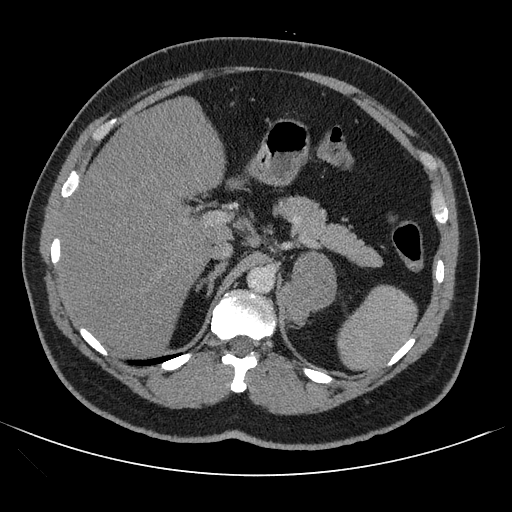
Contrast-enhanced abdominal CT, one axial slice. Slice 72 of 121 in the series (ordered by position). 120 kVp. Intravenous contrast given. Soft-tissue window (W 400 / L 40 HU). 2.5 mm slice thickness. 512 × 512 image matrix, field of view 399 × 399 mm. Male patient, age 53 years. From the clinical record (not read from this slice): diagnosis: adrenocortical carcinoma; tumour side: left adrenal; tumour size at pathology: 7.9 cm; Ki-67 index: 20 %; stage (as recorded): 2.
Structures marked on this image (semi-automatically segmented with operator editing):
- mass: box from (x=282, y=255) to (x=336, y=325) px